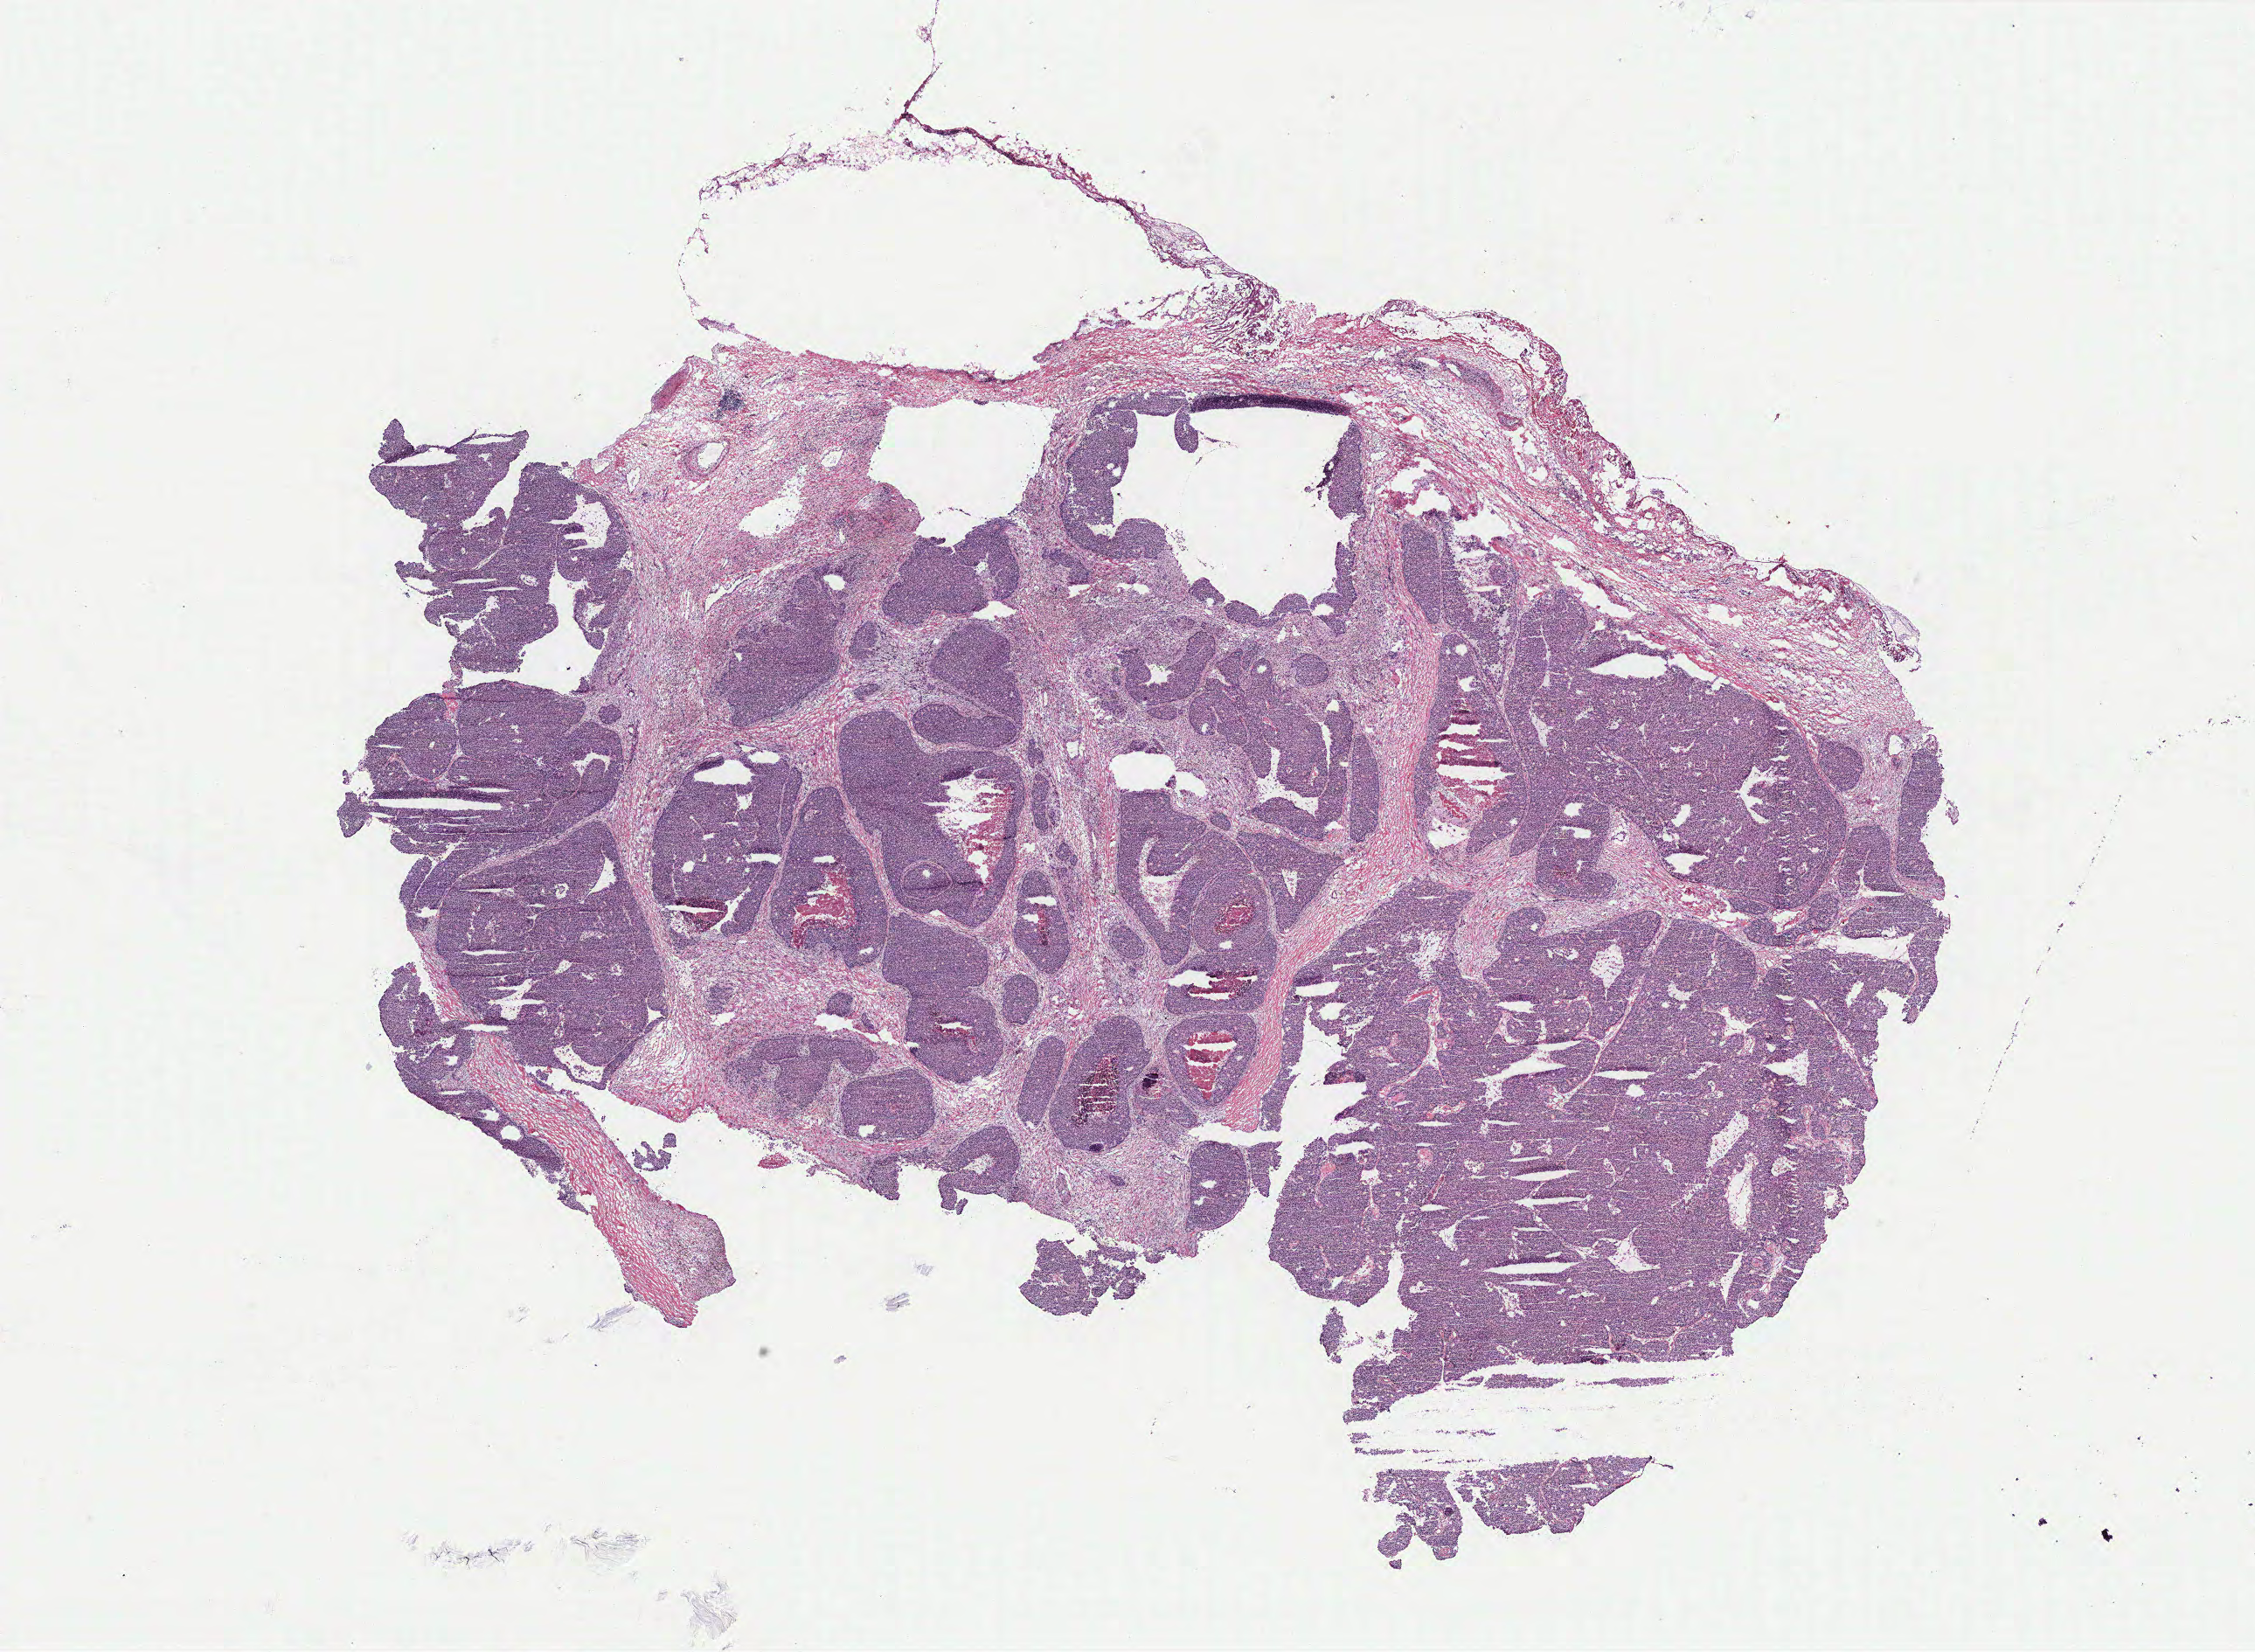
Whole-slide histology image, H&E-stained, low-resolution overview of the scanned area, about 20.6 x 15.1 mm, breast, tumour tissue. Patient: female, age 46 years.
AJCC pathologic stage: IIIB. Diagnosis: Infiltrating duct carcinoma, NOS.